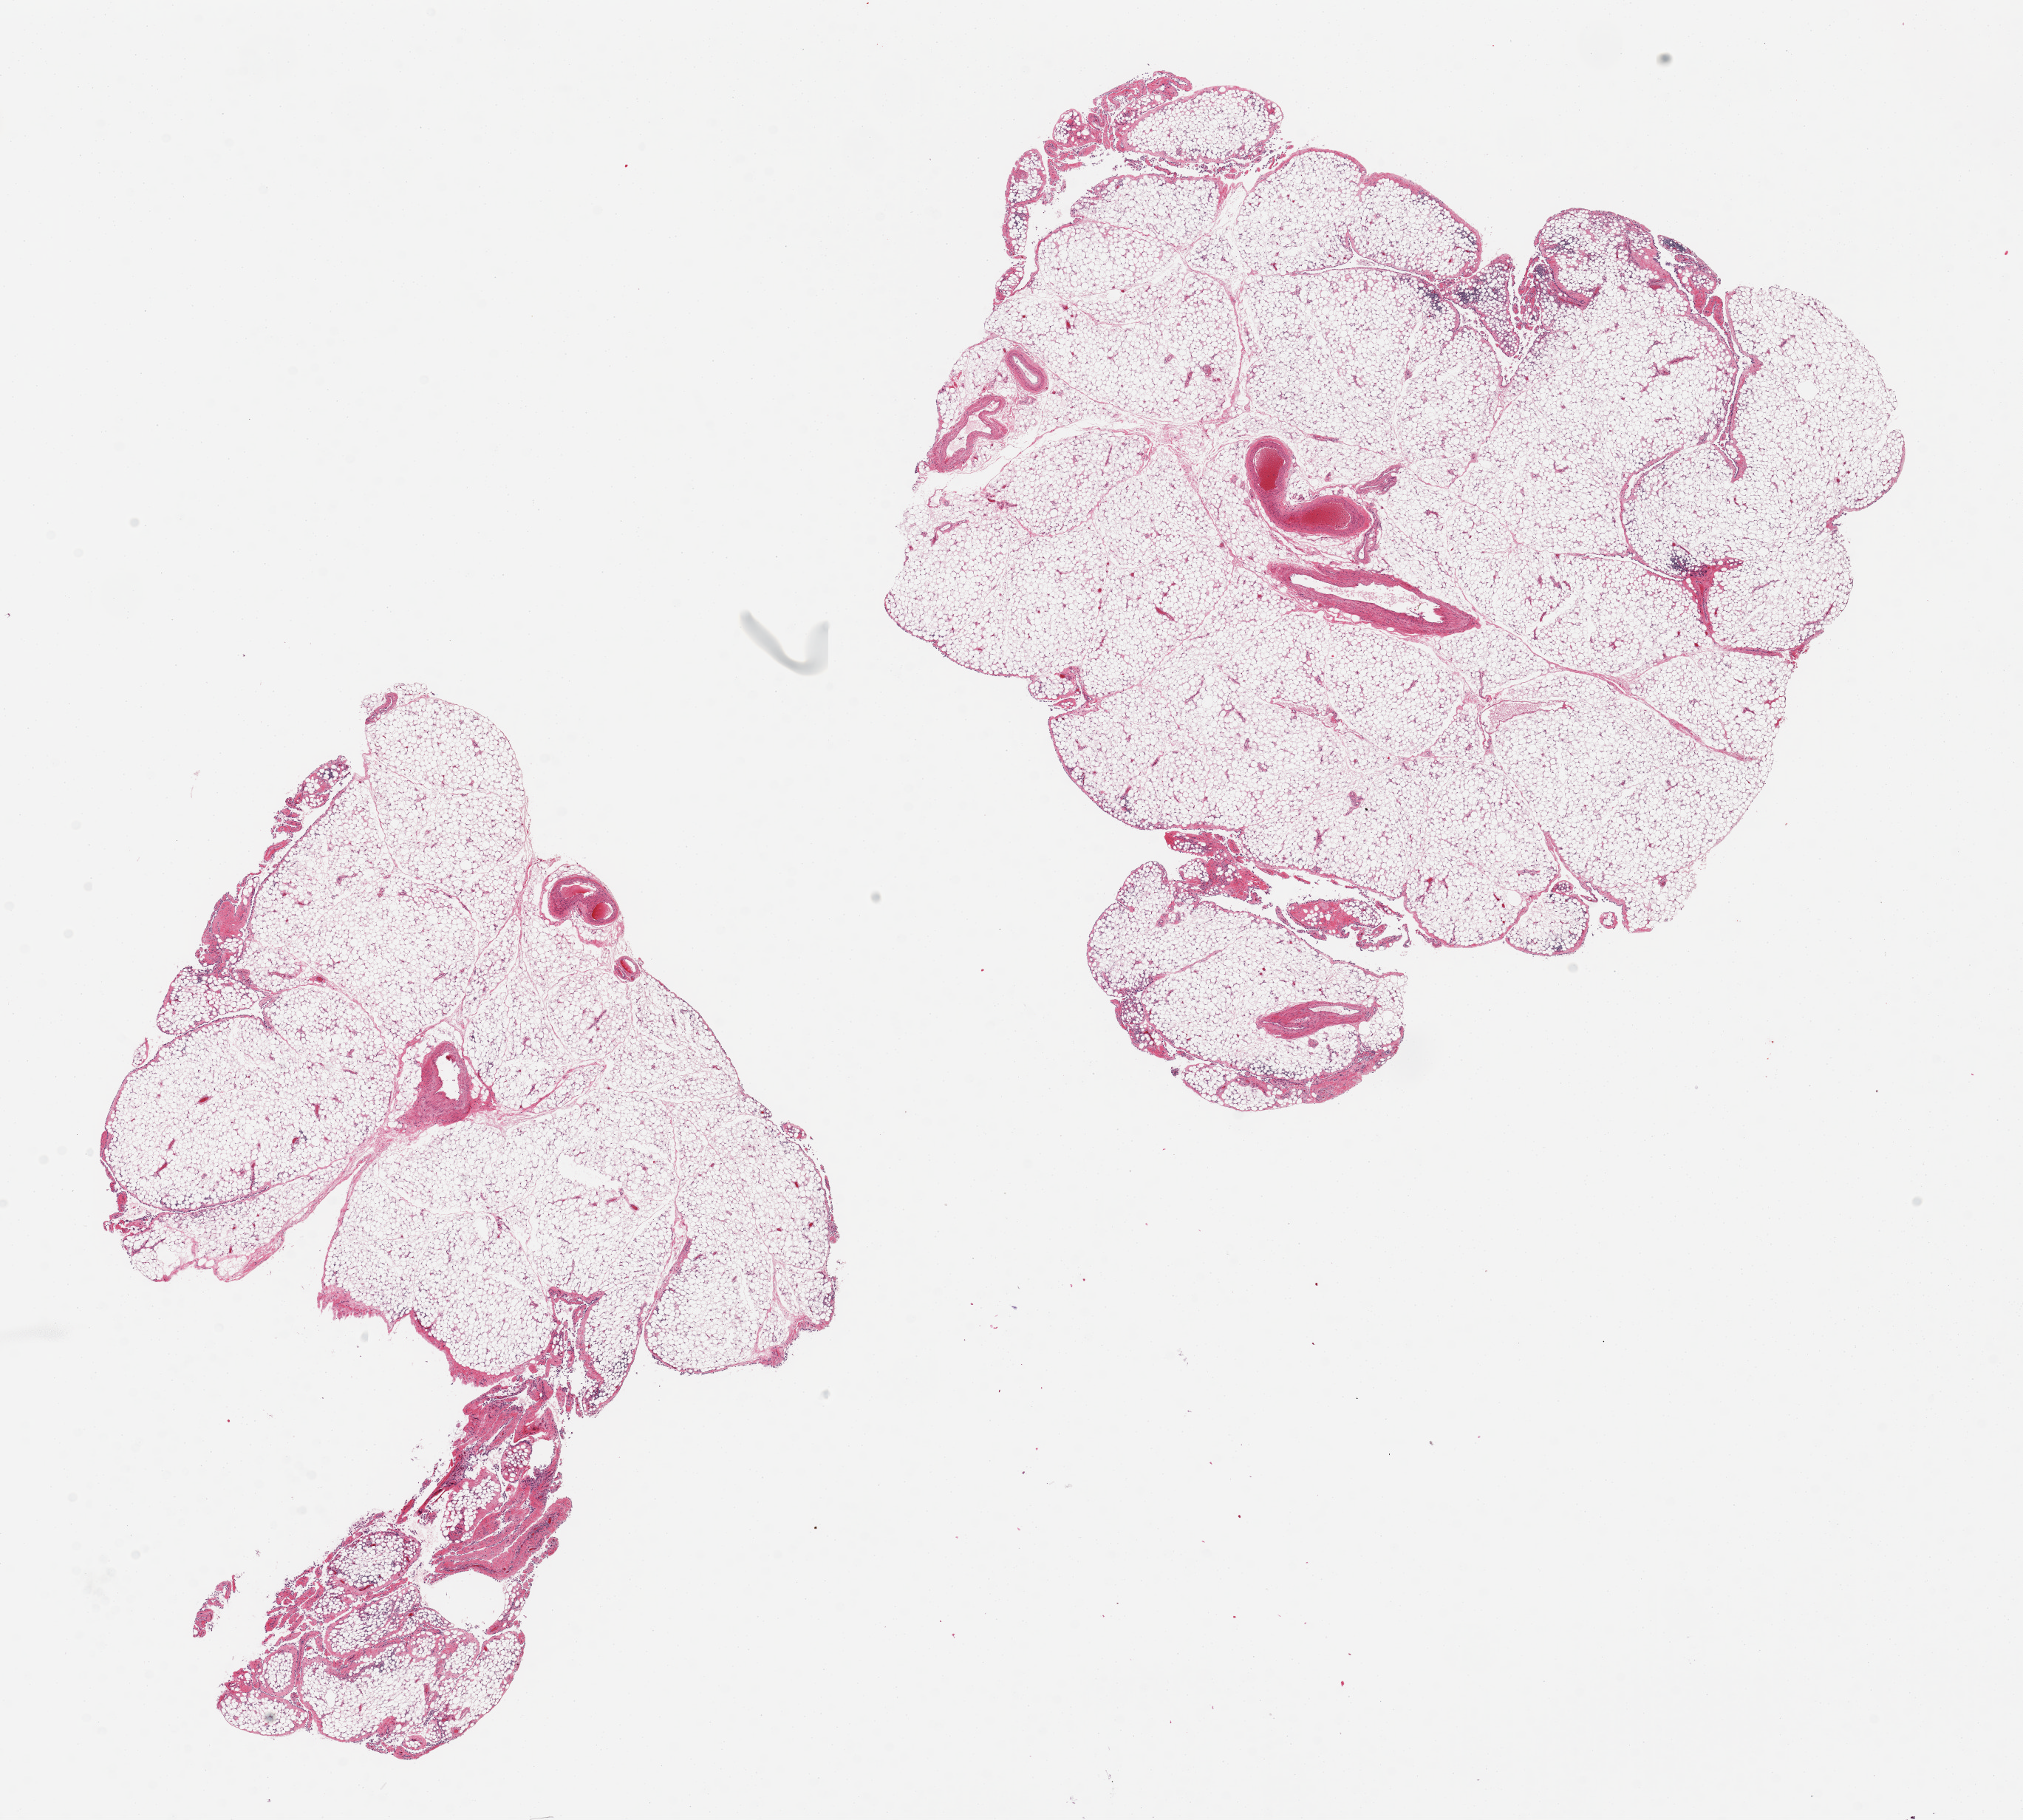
Whole-slide image, hematoxylin and eosin (H&E) stain, shown as a low-resolution overview of the whole scanned area (about 21.7 x 19.5 mm, acquisition: 20x scan); PAXgene-fixed paraffin-embedded (PFPE) section; target tissue: omentum; donor tissue sample.
Review note (as recorded): 2 pieces.